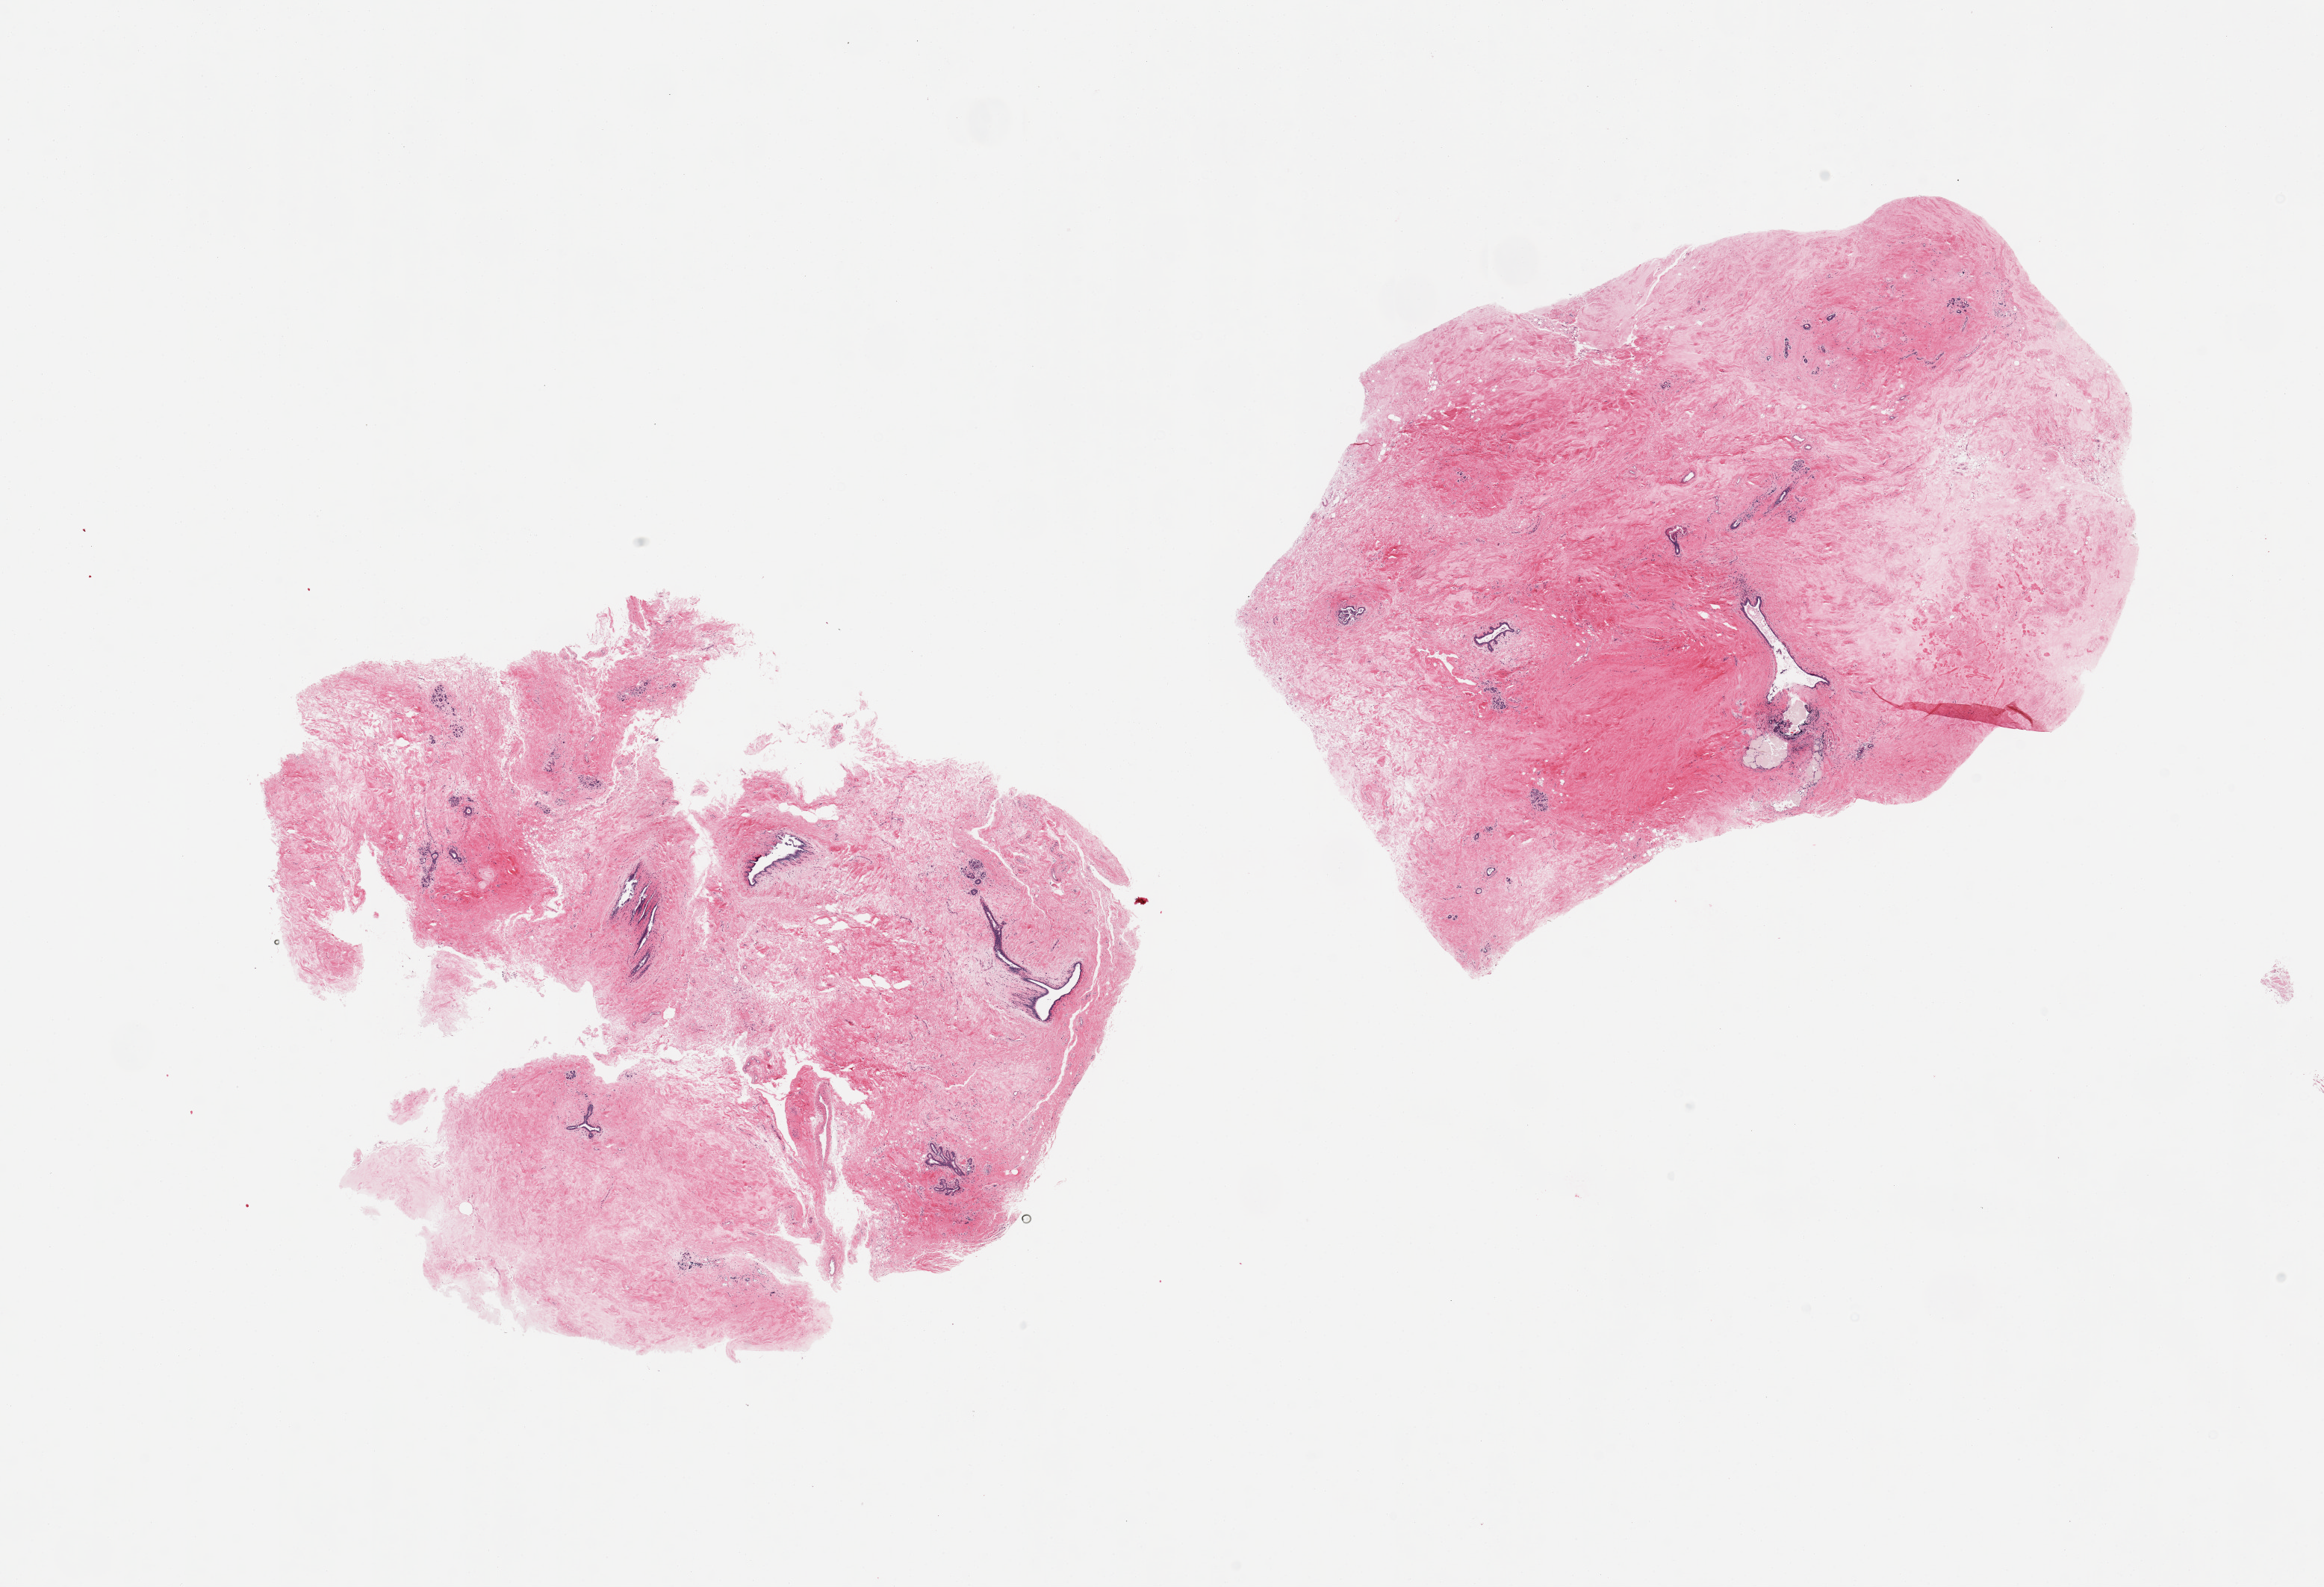
Hematoxylin and eosin (H&E) whole-slide image, brightfield — shown as a low-resolution overview of the whole scanned area (about 24.6 x 16.8 mm, slide scanned at 20x), PAXgene-fixed paraffin-embedded (PFPE) section, target tissue: breast, donor tissue sample. Donor sex: female.
* review note (as recorded): 2 pieces ematous-appearing fibrous mastopathy, rare atrophic TDLUs noted